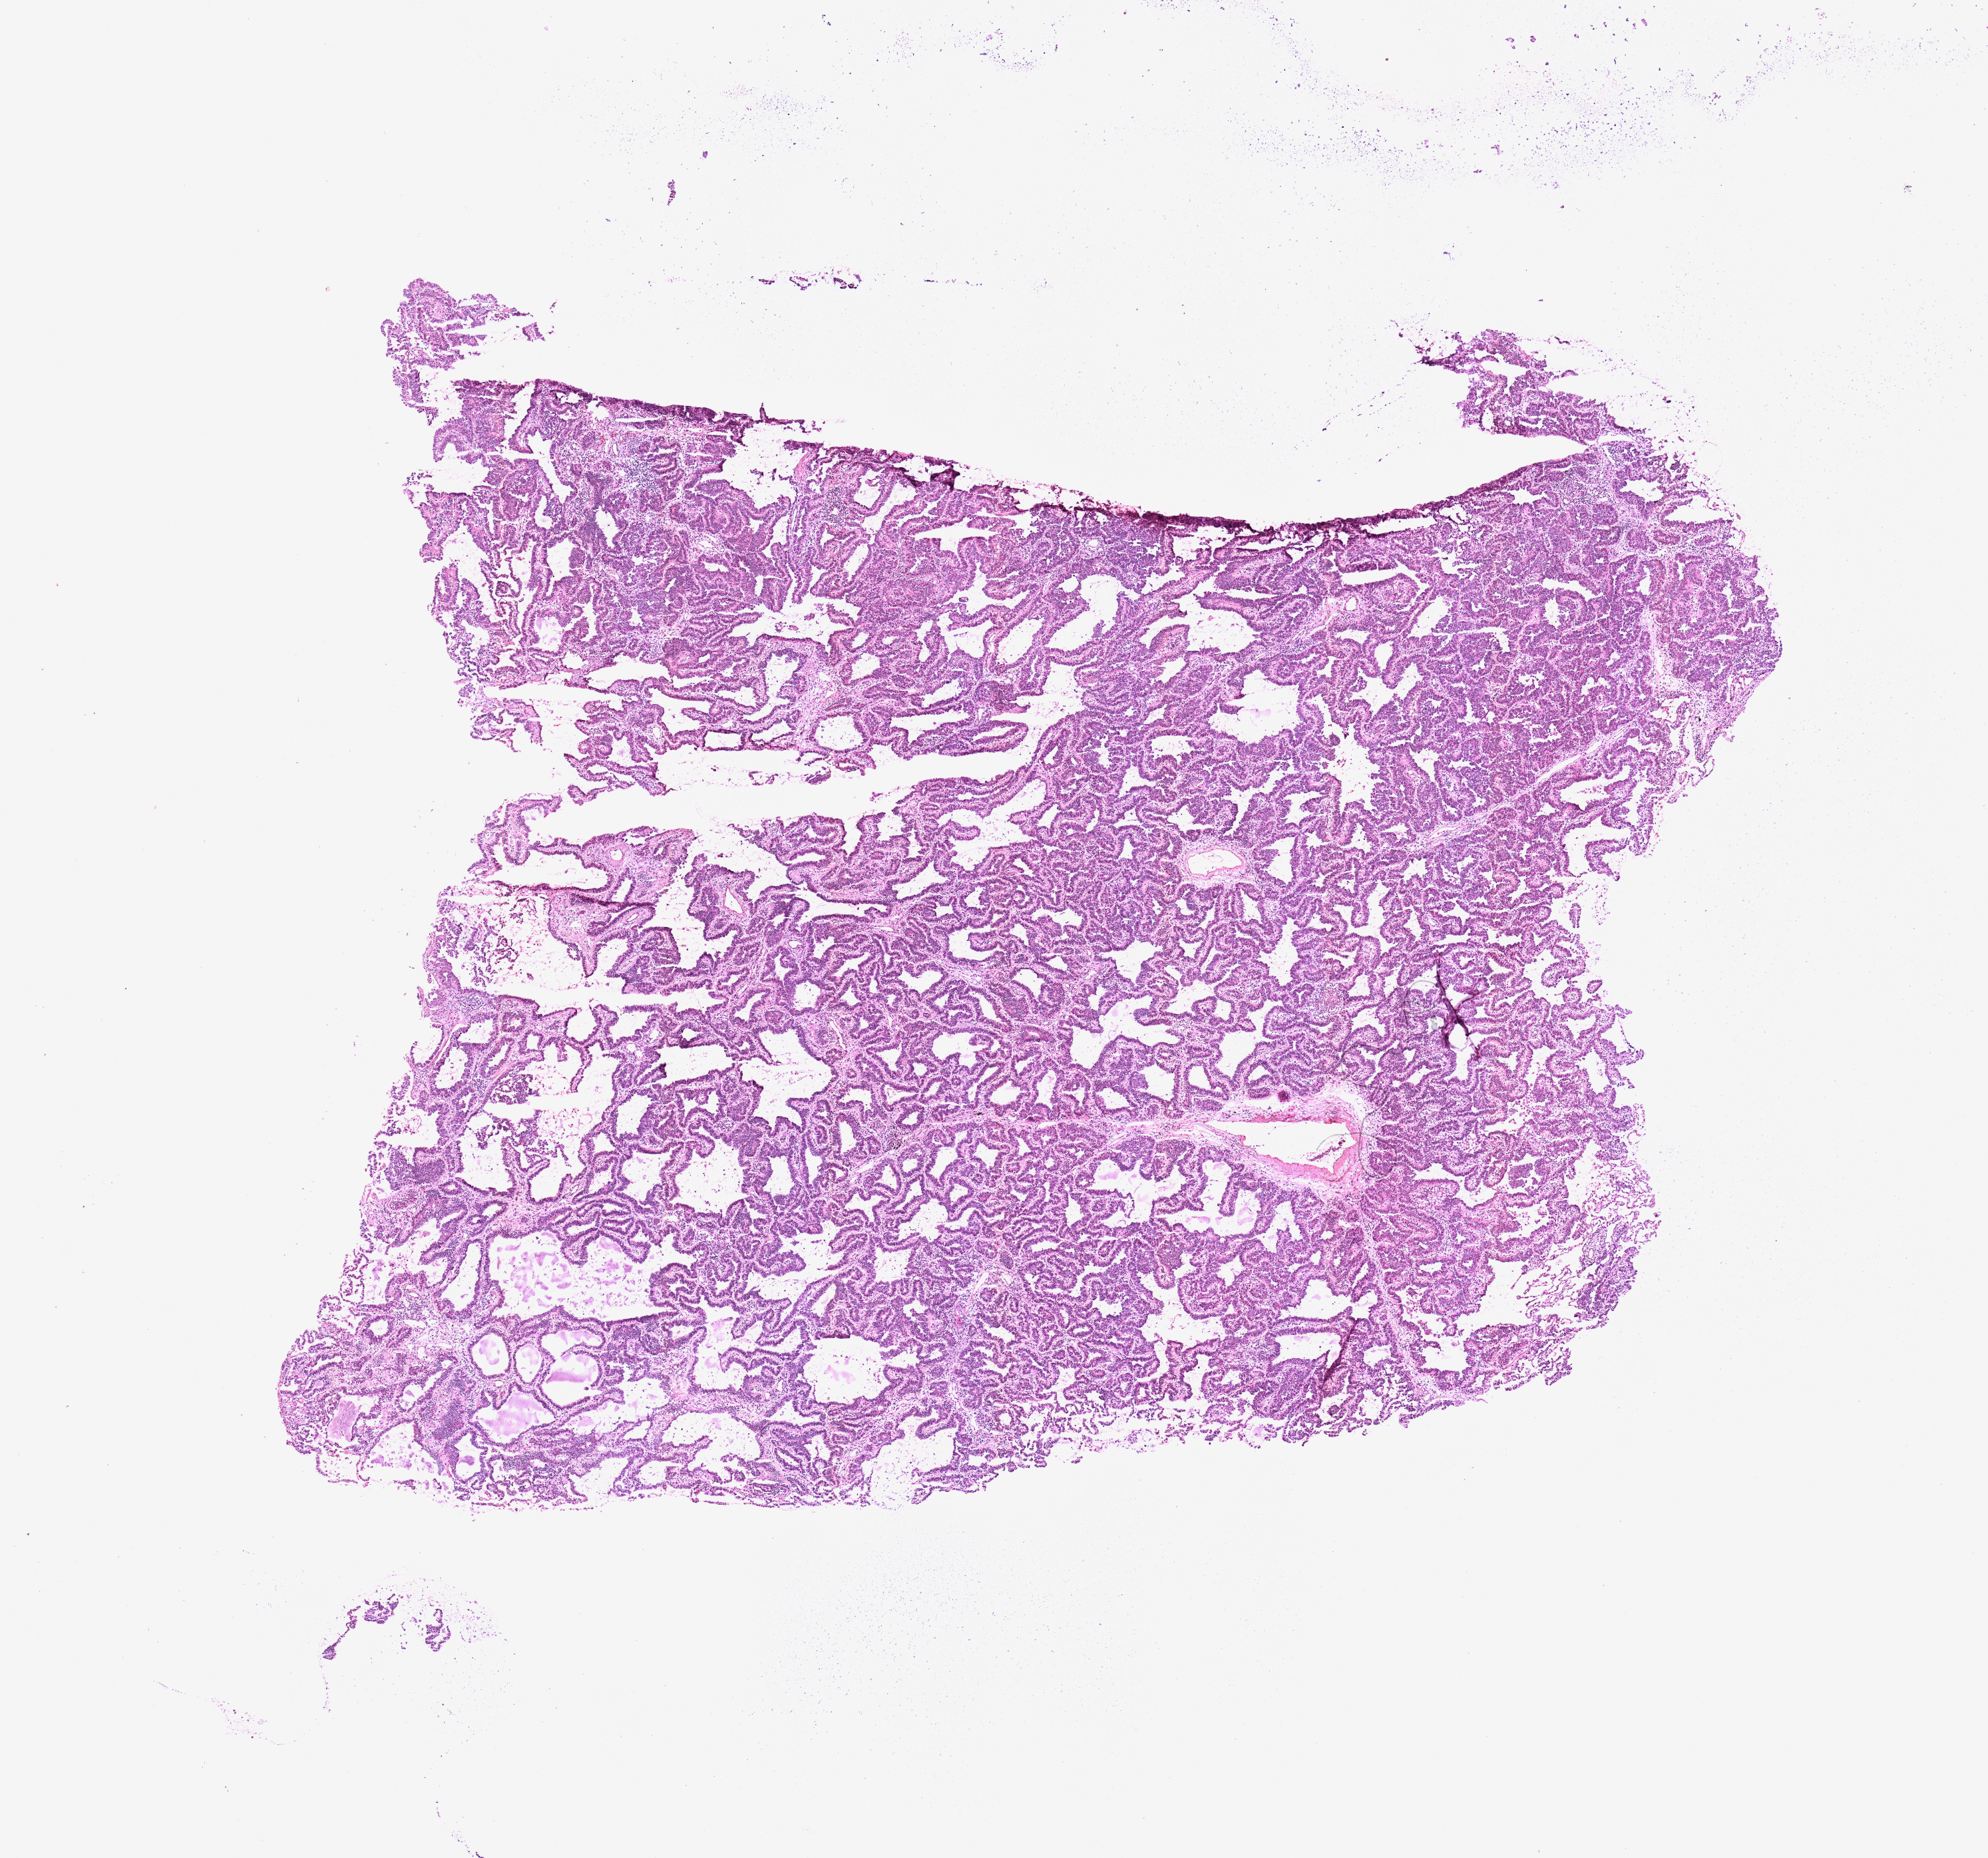
Digitized Hematoxylin and eosin (H&E) stained tissue section (whole slide), a low-resolution overview of the entire scanned area, about 11.8 x 11.0 mm (acquisition: 20x scan), tumour tissue sample, sampled site: lung. 80-year-old female patient. Histologic grade: G1 (well differentiated). Composition of this section per pathologist review: tumour nuclei 90%, necrosis 0%.
AJCC pathologic stage: IA. Diagnosis: Adenocarcinoma, NOS. Primary tumour site (as recorded): right lower lobe.